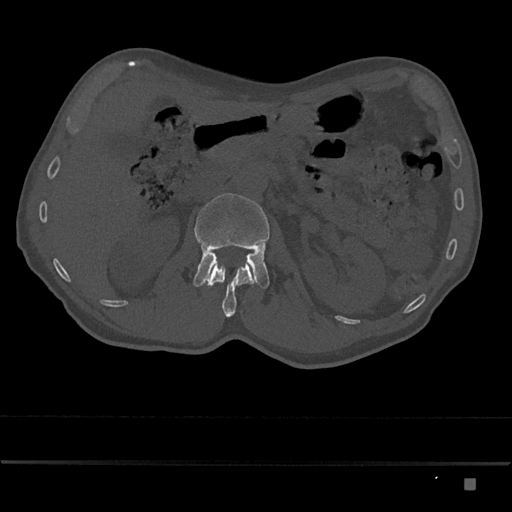
CT including the spine, one axial slice; slice 507 of 797 in the series (ordered by position); 120 kVp; bone window (W 1800 / L 400 HU); 0.5 mm slice thickness; 512 × 512 image matrix, field of view 390 × 390 mm. Male patient, age 72 years. From the clinical record (not read from this slice): primary cancer: prostate.
Annotated regions visible in this slice (semi-automatic segmentation, software-assisted and operator-edited):
- L1 vertebra: bounding box [x1, y1, x2, y2] px = [206, 262, 256, 317]
- L2 vertebra: [193, 193, 270, 289]